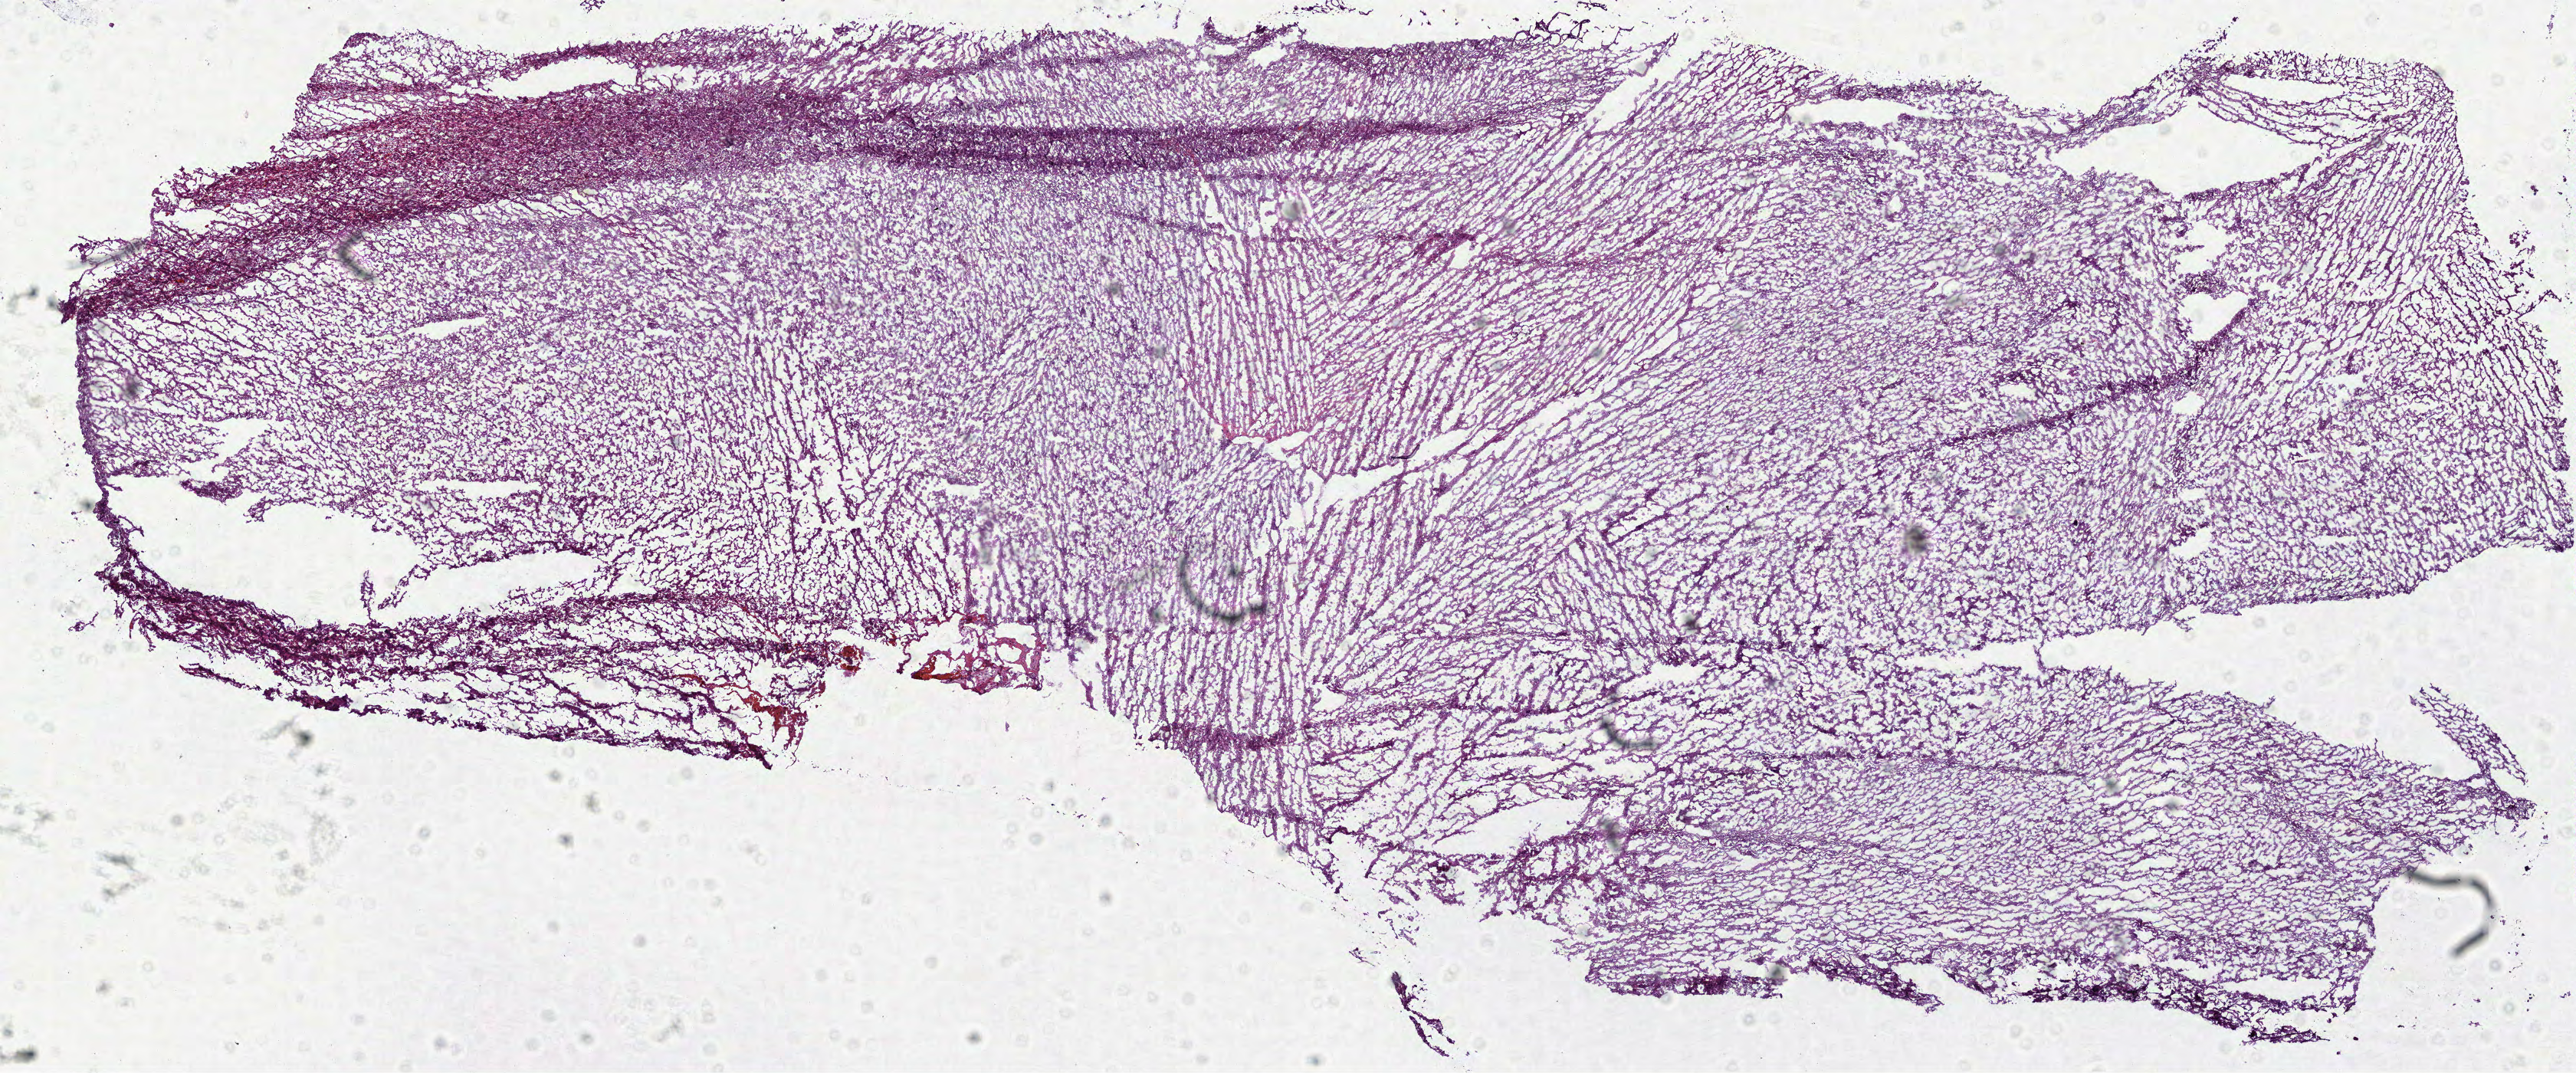
H&E-stained whole-slide image, low-resolution overview of the scanned area, about 13.6 x 5.6 mm. Frozen section from the bottom of the tissue portion. Brain, primary tumour sample. Female patient; age at initial diagnosis 26 years. Histologic grade: G2 (moderately differentiated). Pathologist review of this section (percent, as recorded): tumour cells 100%, tumour nuclei 50%, normal cells 0%, stromal cells 0%, necrosis 0%.
• diagnosis: Oligodendroglioma, NOS